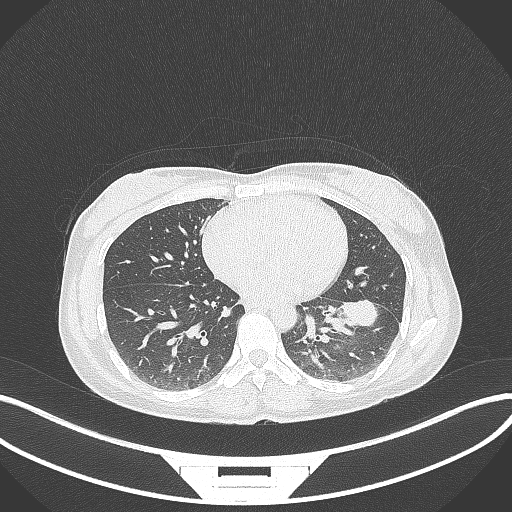
Chest CT, one axial slice; position 30 of 244 along the scan axis; reconstruction kernel B70f; 120 kVp; lung window (W 1500 / L -600 HU); 512 × 512 image matrix, field of view 400 × 400 mm. Female patient, age 41 years. From the clinical record (not read from this slice): clinical TNM (as recorded): T2a N3 M1b.
Outlined on this slice (rectangle marked by the reading radiologist):
- lung tumour (recorded histology: adenocarcinoma): box from (x=335, y=293) to (x=393, y=336) px